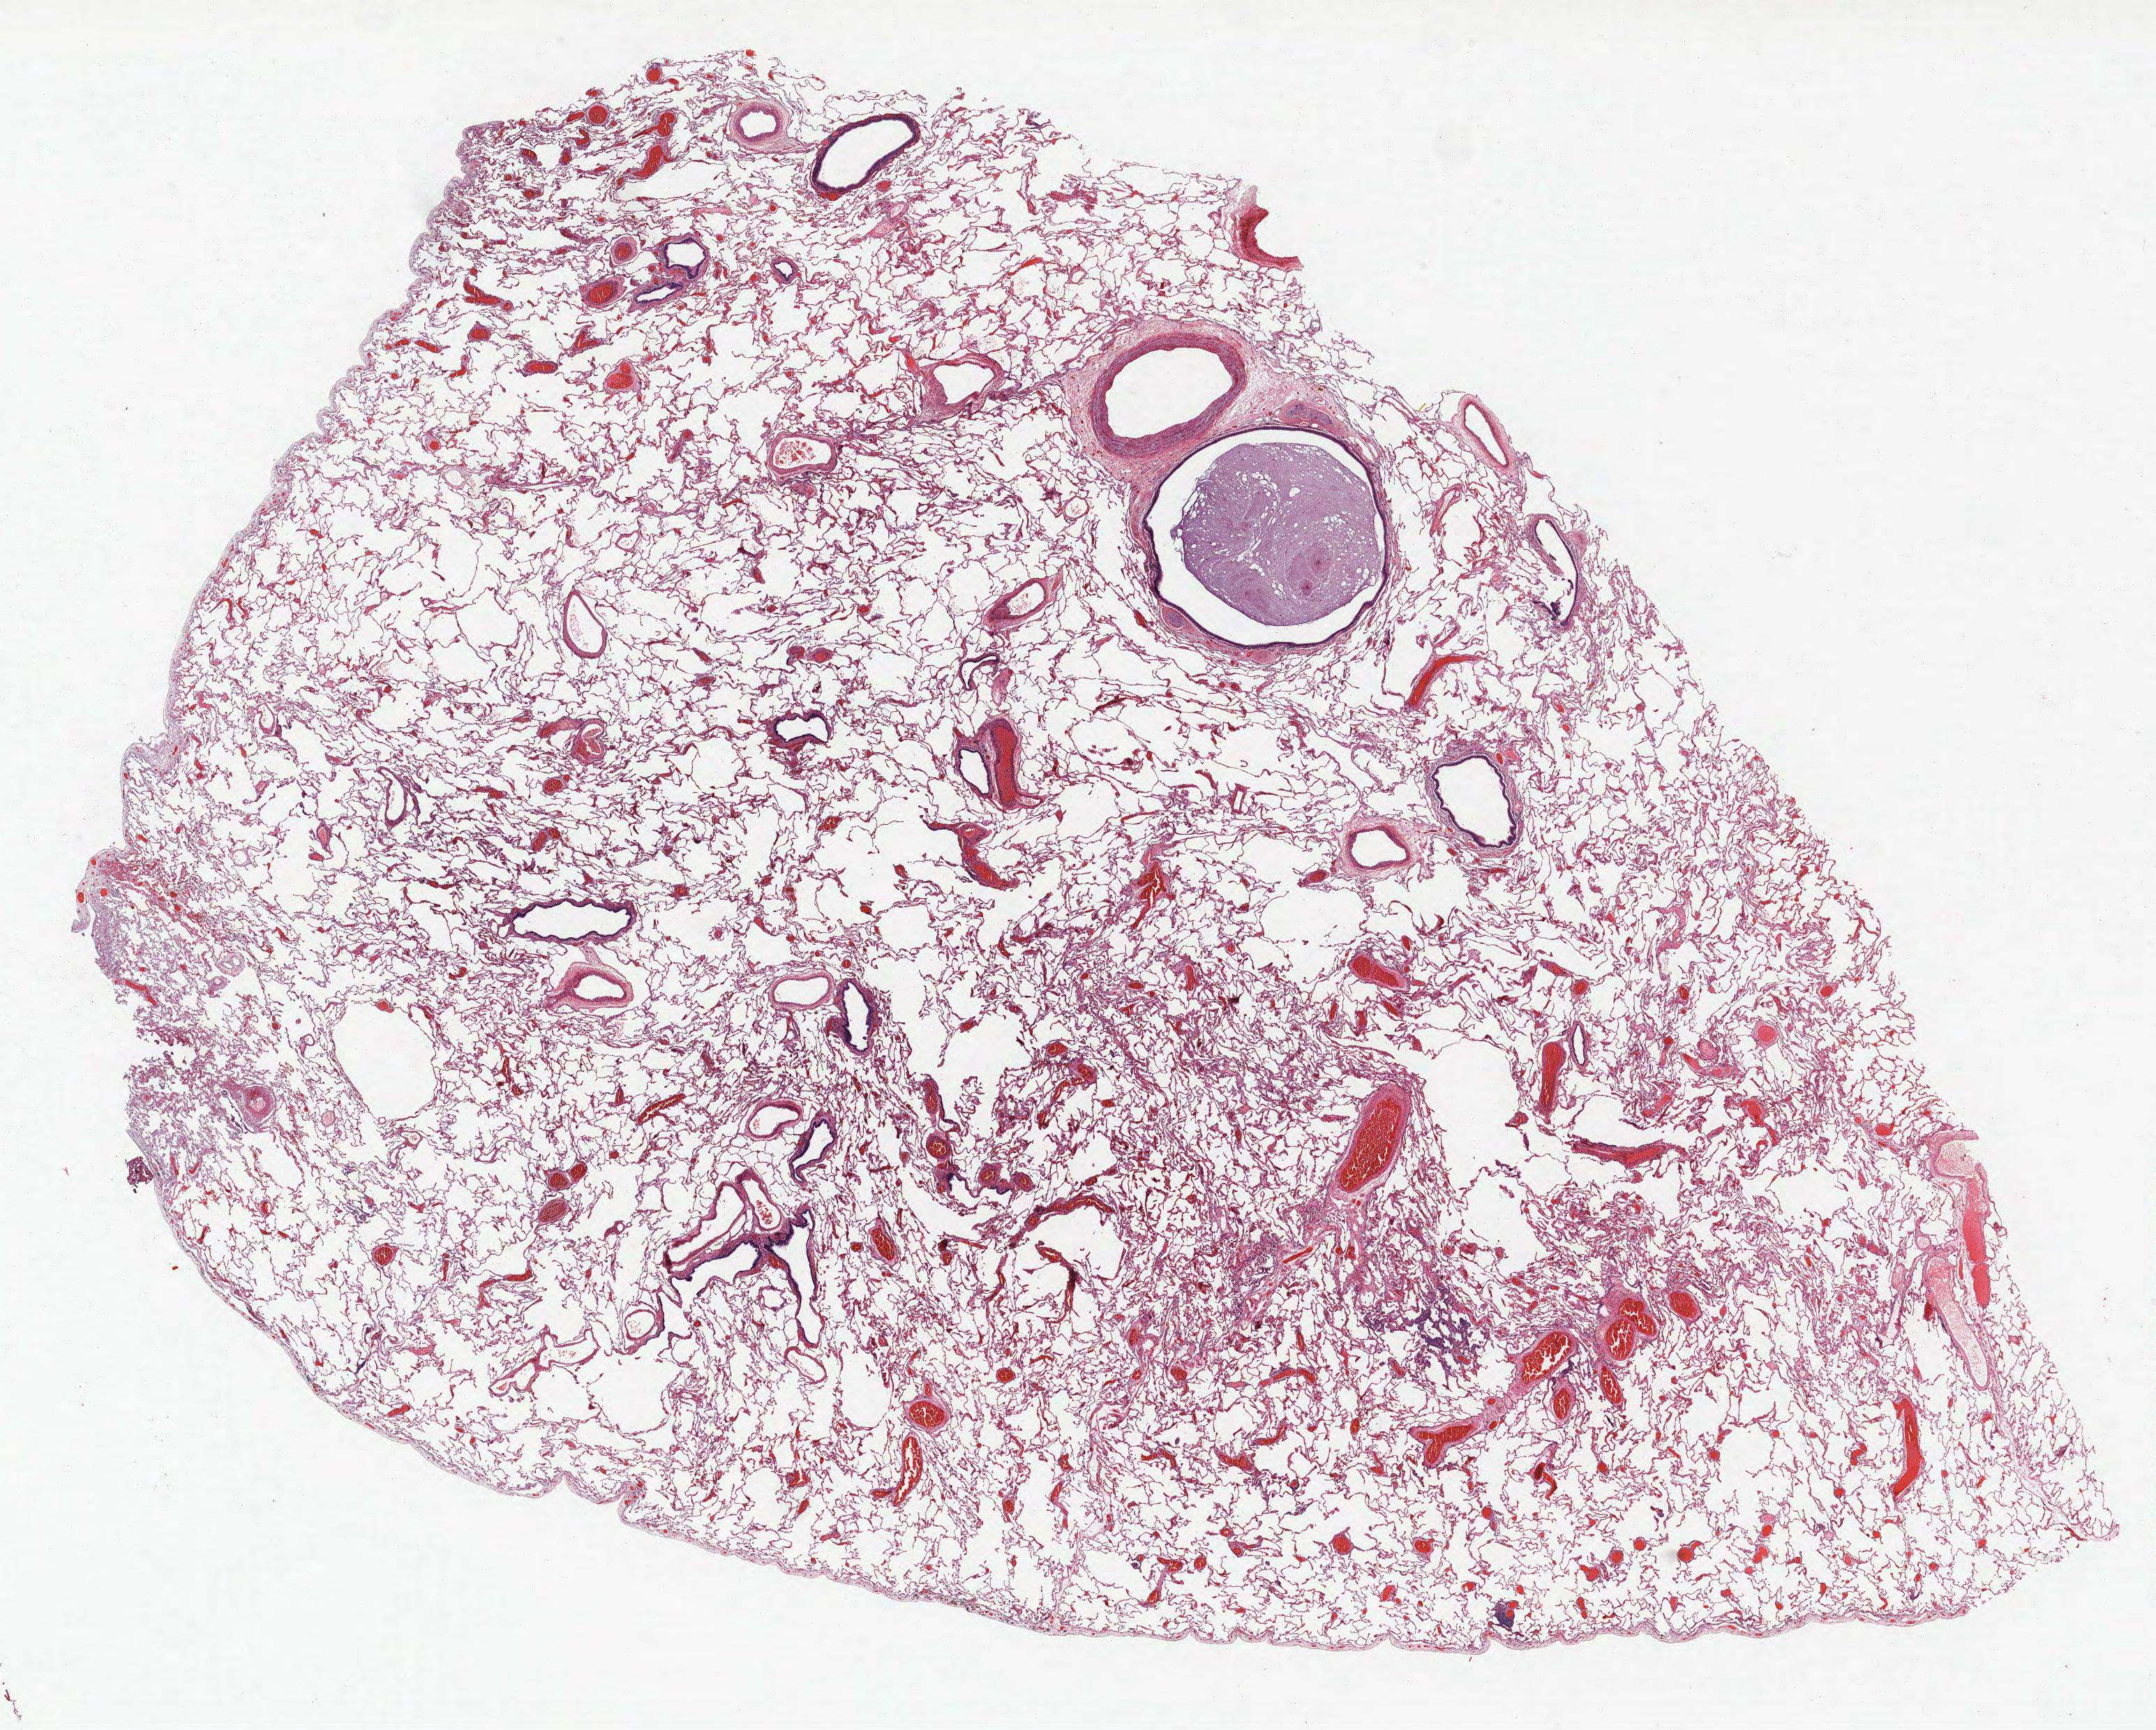
H&E whole-slide image, a low-resolution overview of the entire scanned area, about 24.7 x 19.8 mm, formalin-fixed paraffin-embedded (FFPE) section, lung tissue. Female, age 65 at enrolment. Former smoker at enrolment. Grade: moderately differentiated (G2).
* participant's lung-cancer diagnosis: Adenocarcinoma, NOS
* stage (AJCC 6th edition): IA
* primary tumour location (clinical record): left upper lobe
* tumour size (pathology): 30 mm
* ICD-O-3 topography: upper lobe of lung (C34.1)